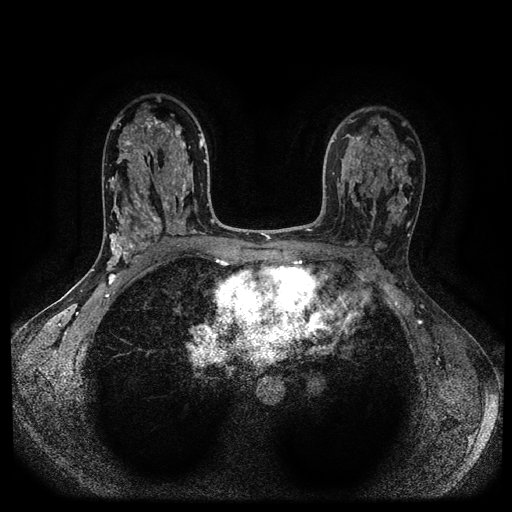
Breast MRI (dynamic contrast-enhanced, multi-phase), one axial slice; position 64 of 116 along the scan axis; dynamic contrast-enhanced series, time point 2 of 5 at this slice position (early post-contrast); 1.5 T; TE 2.6 ms, TR 5.4 ms; 2 mm slice thickness; 512 × 512 image matrix, field of view 340 × 340 mm. Female patient, age 43 years.
Annotated regions visible in this slice (semi-automatically segmented with operator editing):
- breast lesion (labelled benign in the annotation): box from (x=149, y=212) to (x=164, y=239) px